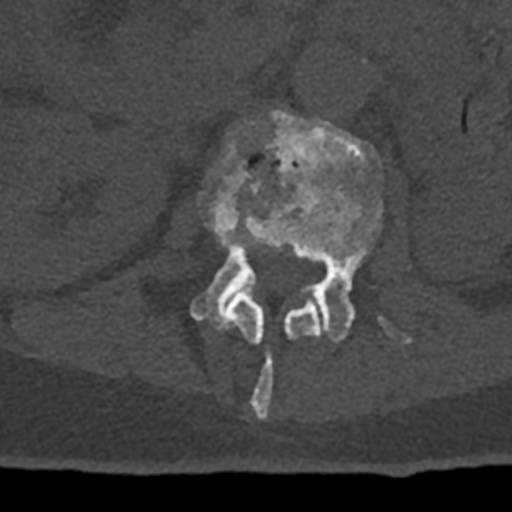
CT including the spine, one axial slice. Slice 402 of 797 in the series (ordered by position). Reconstruction kernel Br40s/3. 120 kVp. Bone window (W 1800 / L 400 HU). 0.5 mm slice thickness. 512 × 512 image matrix, field of view 160 × 160 mm. Patient: male, 74 years. Case-level facts recorded for this patient, not image findings: primary cancer: renal; vertebrae with lytic lesions (as recorded): T10, L1, L2, L3, L4, L5.
Outlined on this slice (semi-automatically segmented with operator editing):
- L1 vertebra: bounding box [x1, y1, x2, y2] px = [203, 134, 320, 419]
- L2 vertebra: [190, 110, 411, 344]